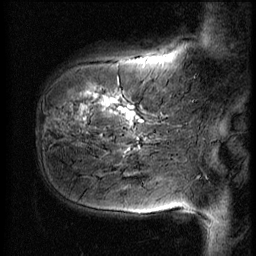
Breast MRI (dynamic contrast-enhanced), one sagittal slice. Position 13 of 56 along the scan axis. 3 images stored at this slice position (order not interpretable as contrast timing). 1.5 T. TE 4.2 ms, TR 9 ms. 2.5 mm slice thickness. 256 × 256 image matrix, field of view 180 × 180 mm. Female patient, age 51 years. Case-level facts recorded for this patient, not image findings: setting: breast cancer imaged before/during neoadjuvant chemotherapy; receptor status: HR-positive, HER2-negative.
Outlined on this slice (semi-automatically segmented with operator editing):
- analysis volume of interest (the breast-tissue region the enhancement analysis was run in; not a lesion): bounding box <41,58,167,161> (left, top, right, bottom; pixels)
- tumour enhancement mask (voxels above the 140 % enhancement threshold inside the analysis volume of interest): <71,92,142,125>